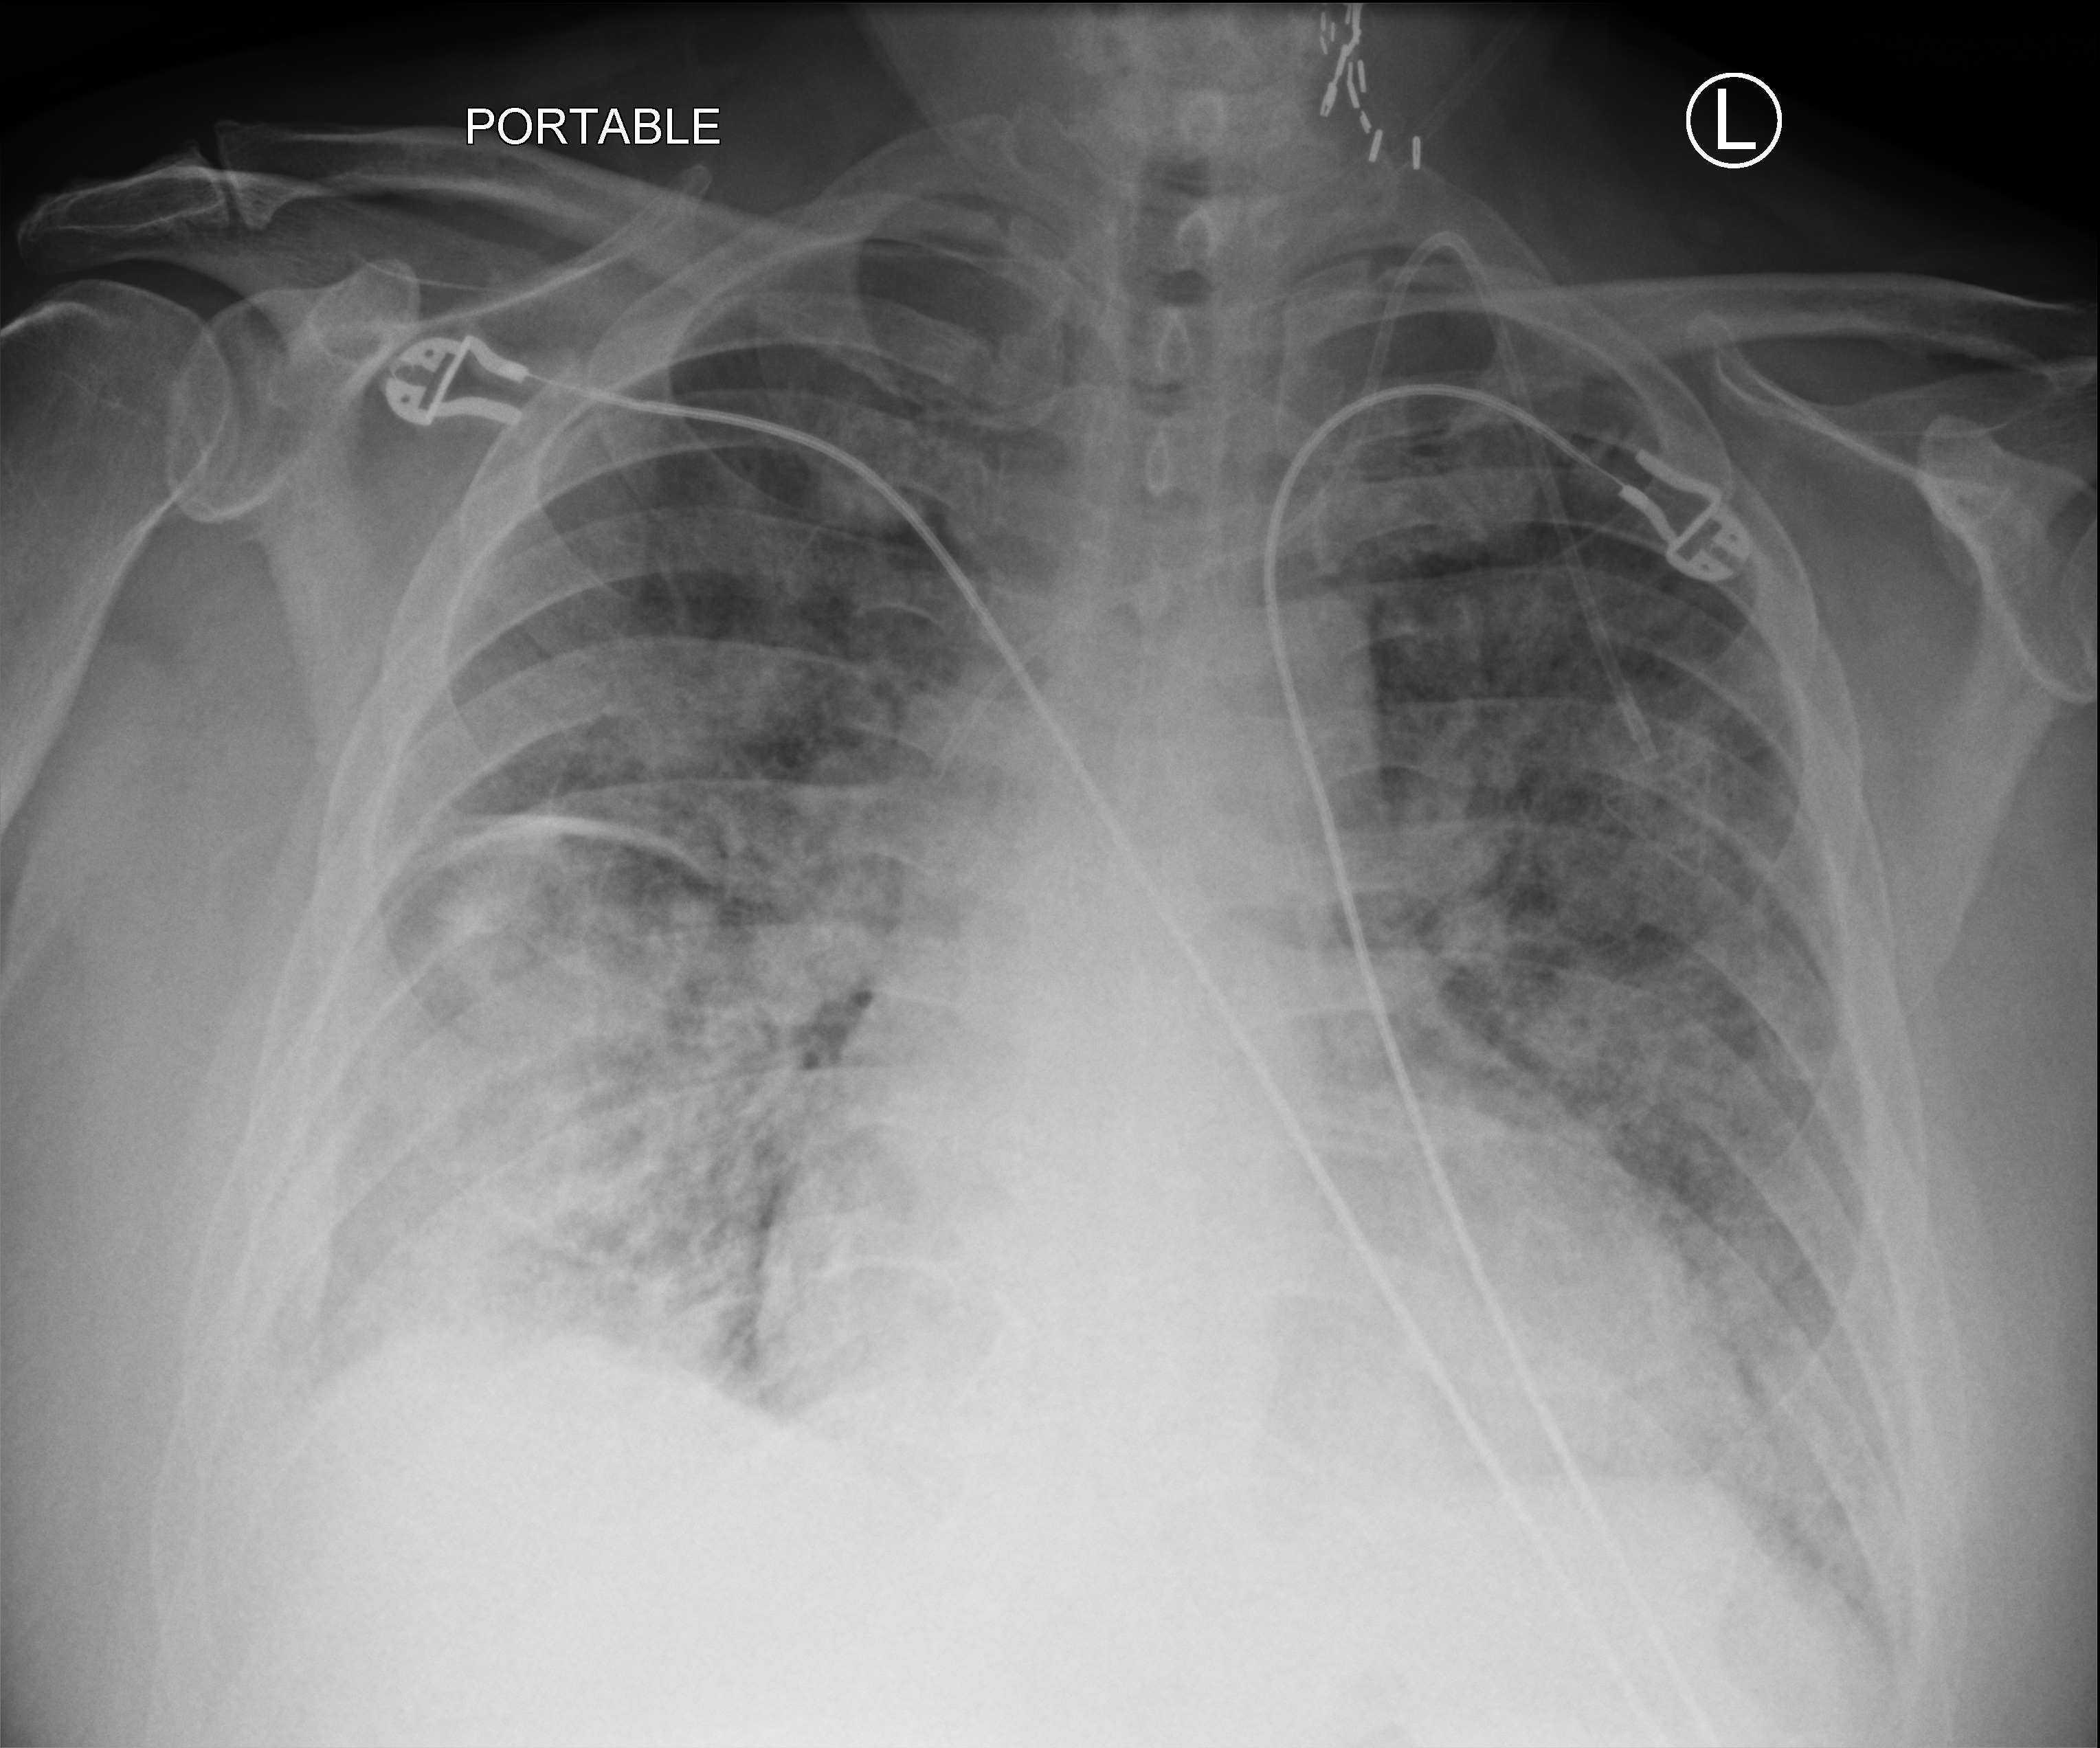
Chest X-ray (portable), anteroposterior (AP) projection. Male patient hospitalised with COVID-19, age 60–74 years.
Hospital-stay facts (about this admission, not read from this image; timing relative to this image not recorded): admitted to intensive care during this hospital stay: no; length of hospital stay: 4 days; mechanically ventilated during this hospital stay: no.